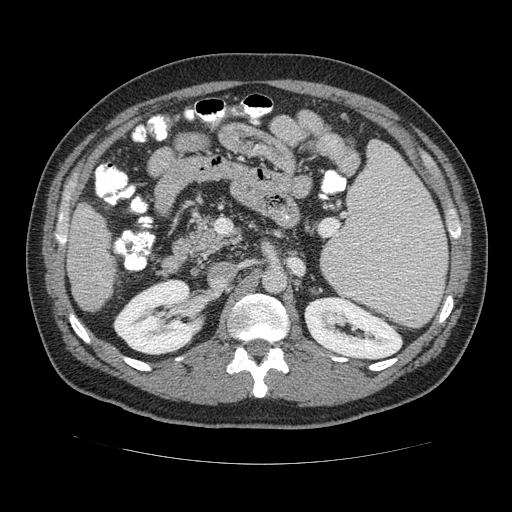
Contrast-enhanced abdominal CT (liver protocol), one axial slice; slice 57 of 113 in the series (ordered by position); reconstruction kernel STANDARD; soft-tissue window (W 400 / L 40 HU); 2.5 mm slice thickness; 512 × 512 image matrix, field of view 400 × 400 mm. From the clinical record (not read from this slice): diagnosis: hepatocellular carcinoma (patient treated with transarterial chemoembolisation; whether this scan precedes or follows treatment is not stated here); TNM stage (as recorded): Stage-II; Child-Pugh class: B; tumour differentiation: moderately differentiated; tumour nodularity: multinodular.
Structures marked on this image (semi-automatically segmented with operator editing):
- liver parenchyma outside the tumour (the mass and vessels are separate outlines, so this box may not span the whole liver): bounding box <66,200,117,312> (left, top, right, bottom; pixels)
- liver vessels: <83,217,86,220>